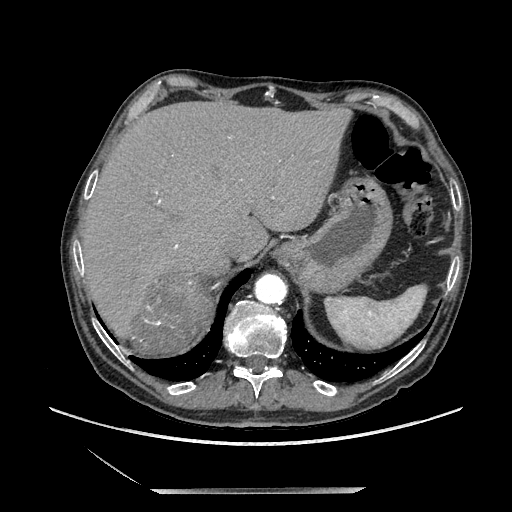
Contrast-enhanced abdominal CT, one axial slice. Position 171 of 243 along the scan axis. Soft-tissue window (W 400 / L 40 HU). 1.25 mm slice thickness. 512 × 512 image matrix. Male patient. Case-level facts recorded for this patient, not image findings: diagnosis: adrenocortical carcinoma; tumour side: right adrenal; tumour size at pathology: 16 cm; Ki-67 index: 17 %.
Outlined on this slice (semi-automatically segmented with operator editing):
- mass: bounding box (x1, y1, x2, y2) in pixels: (133, 274, 212, 354)